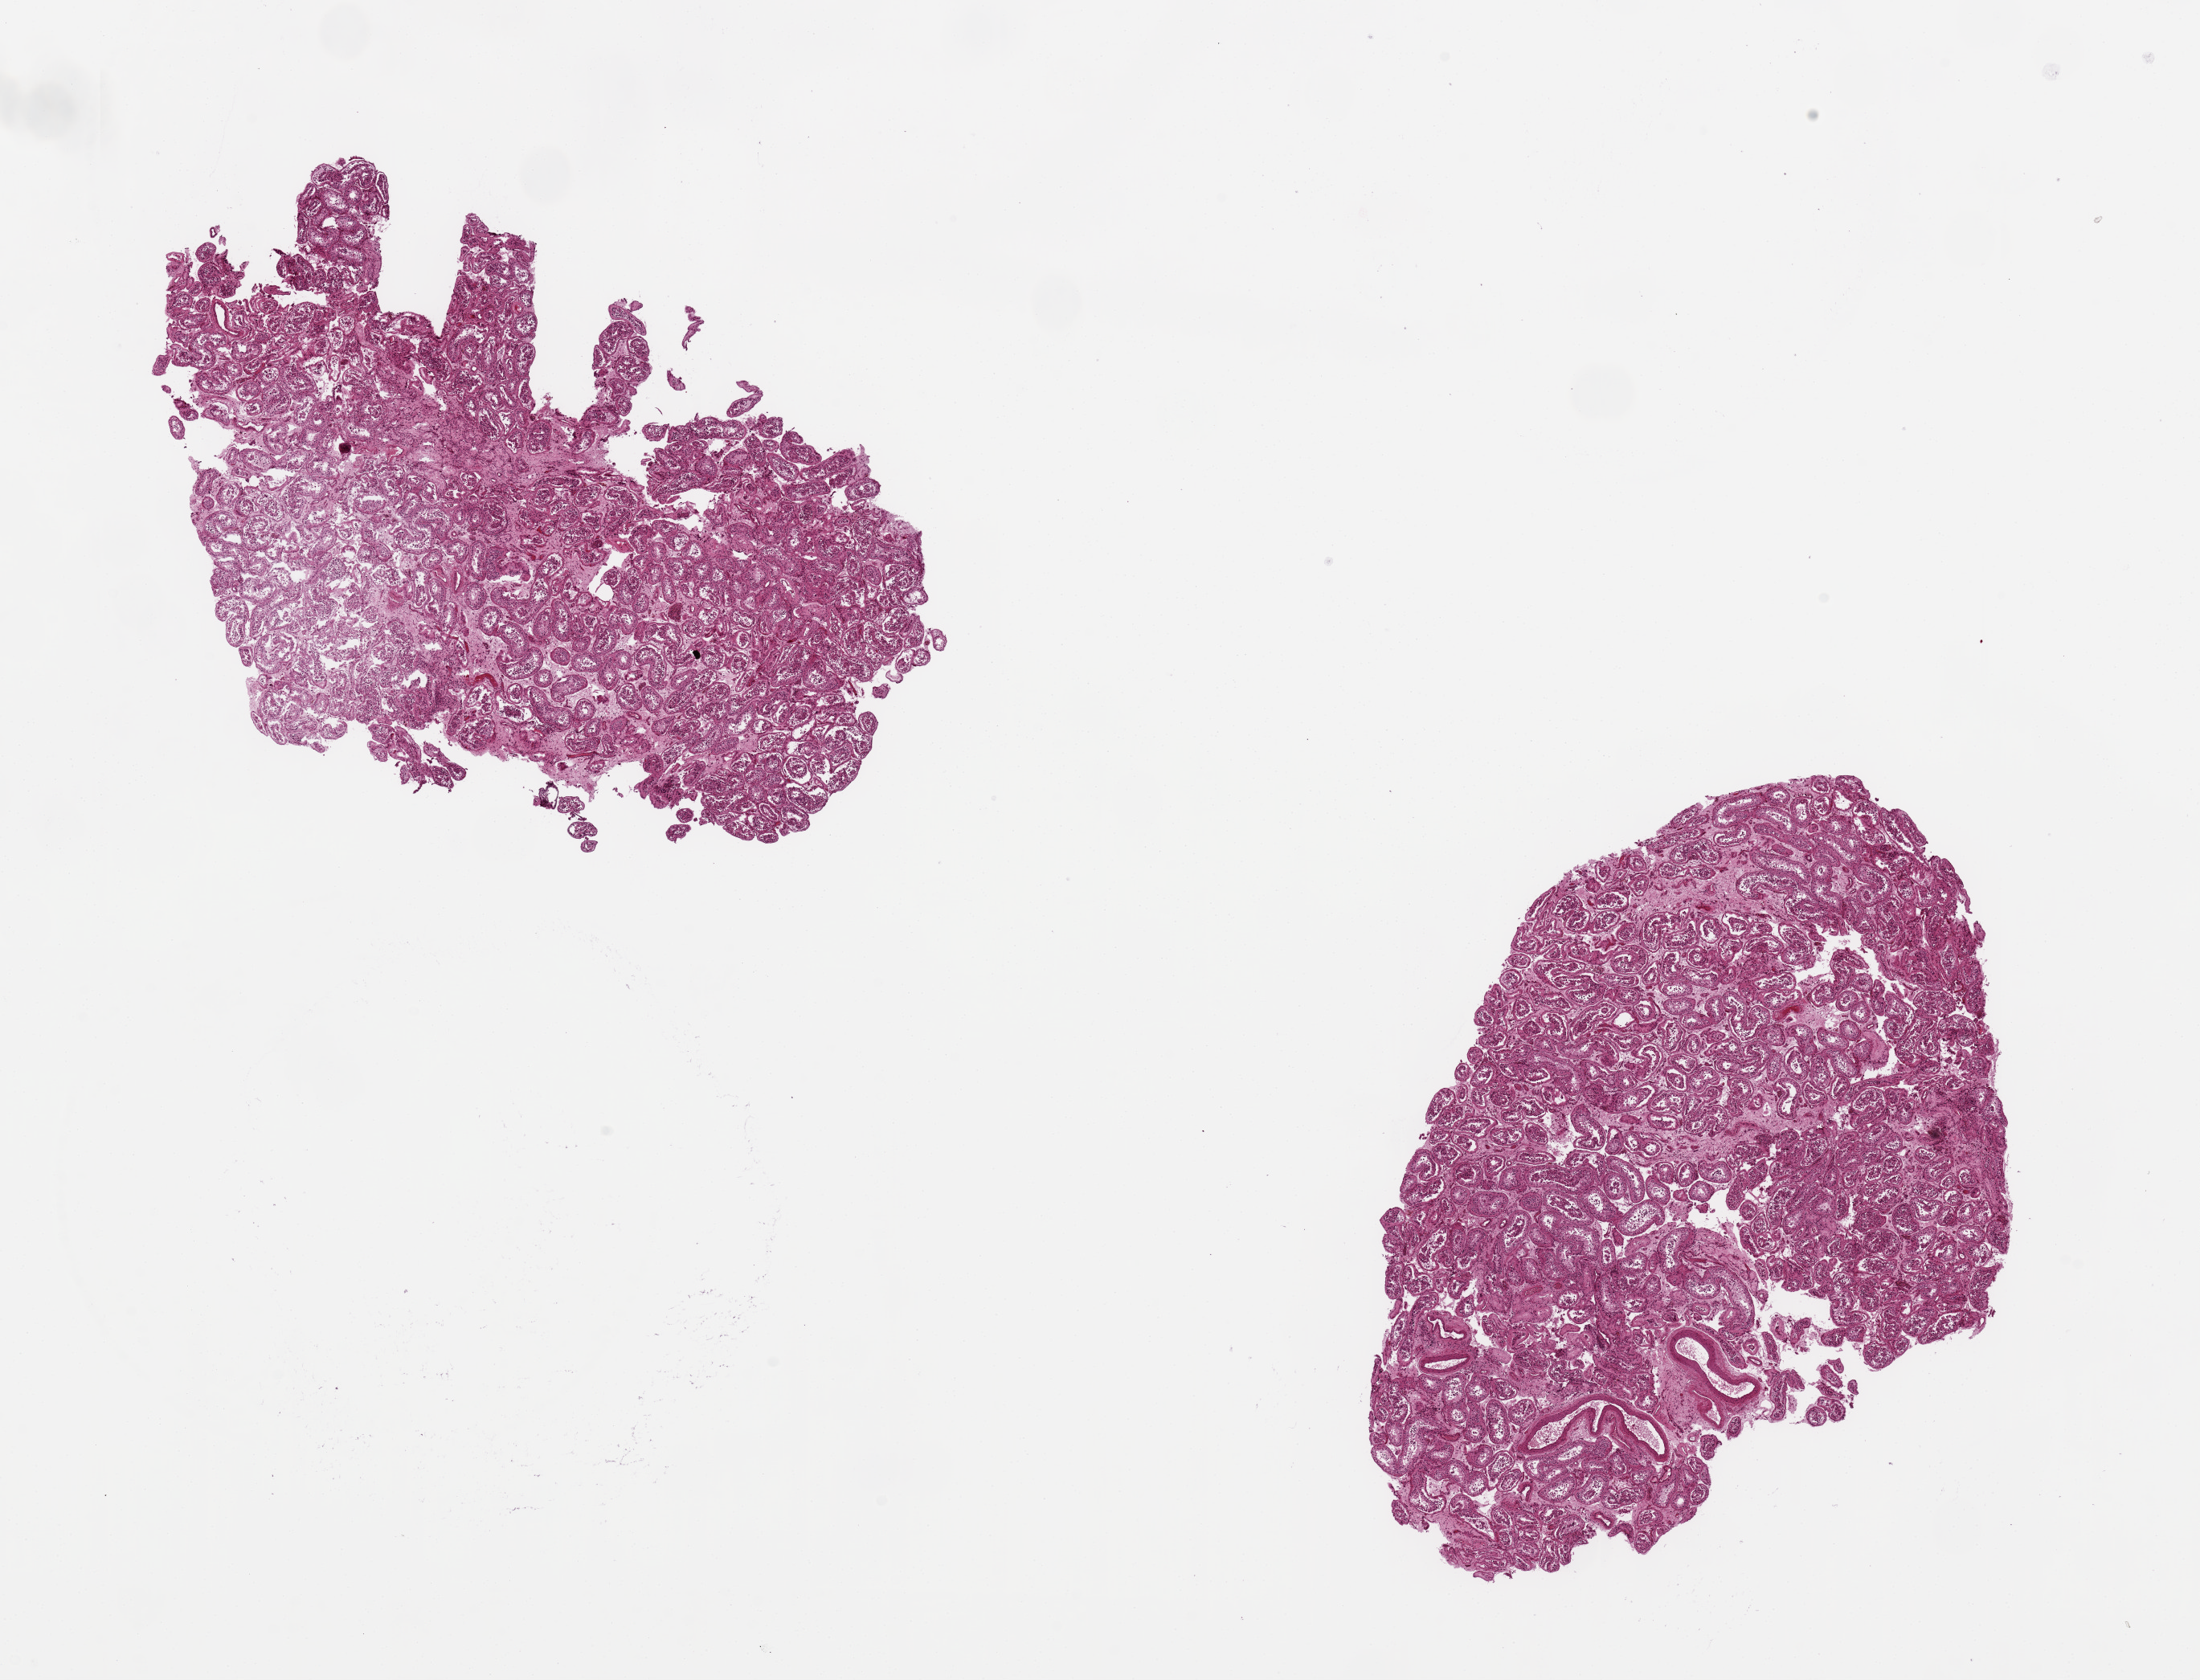
Haematoxylin and eosin whole-slide image, brightfield, shown as a low-resolution overview of the whole scanned area (about 21.7 x 16.5 mm), PAXgene-fixed, paraffin-embedded tissue, sampled site (target tissue): testis, tissue donor sample. Donor sex: male.
Pathologist's review note for this sample: 2 ~8x5mm pieces.